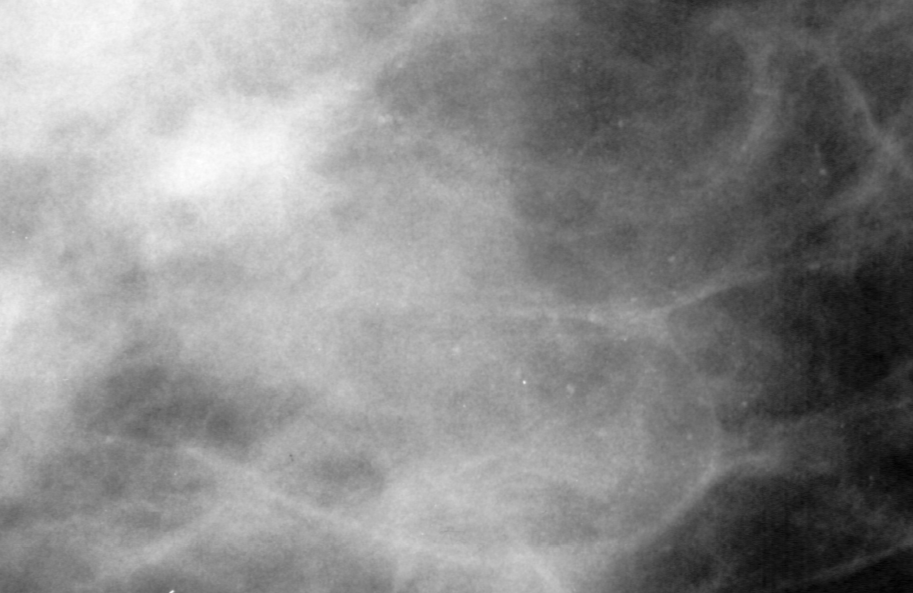
Region of interest cut from a scanned film mammogram (one marked finding); left breast; MLO view; BI-RADS breast density category 4 (scale 1–4).
- Calcifications, morphology punctate, distribution segmental; BI-RADS assessment category 4; pathology (as recorded): benign.